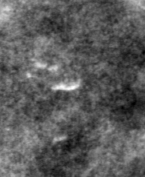
Region of interest cut from a scanned film mammogram (one marked finding), left breast, MLO view, BI-RADS breast density category 4 (scale 1–4).
Calcifications, morphology pleomorphic, distribution clustered; BI-RADS assessment category 4; pathology result (as recorded, not read from the image): benign.